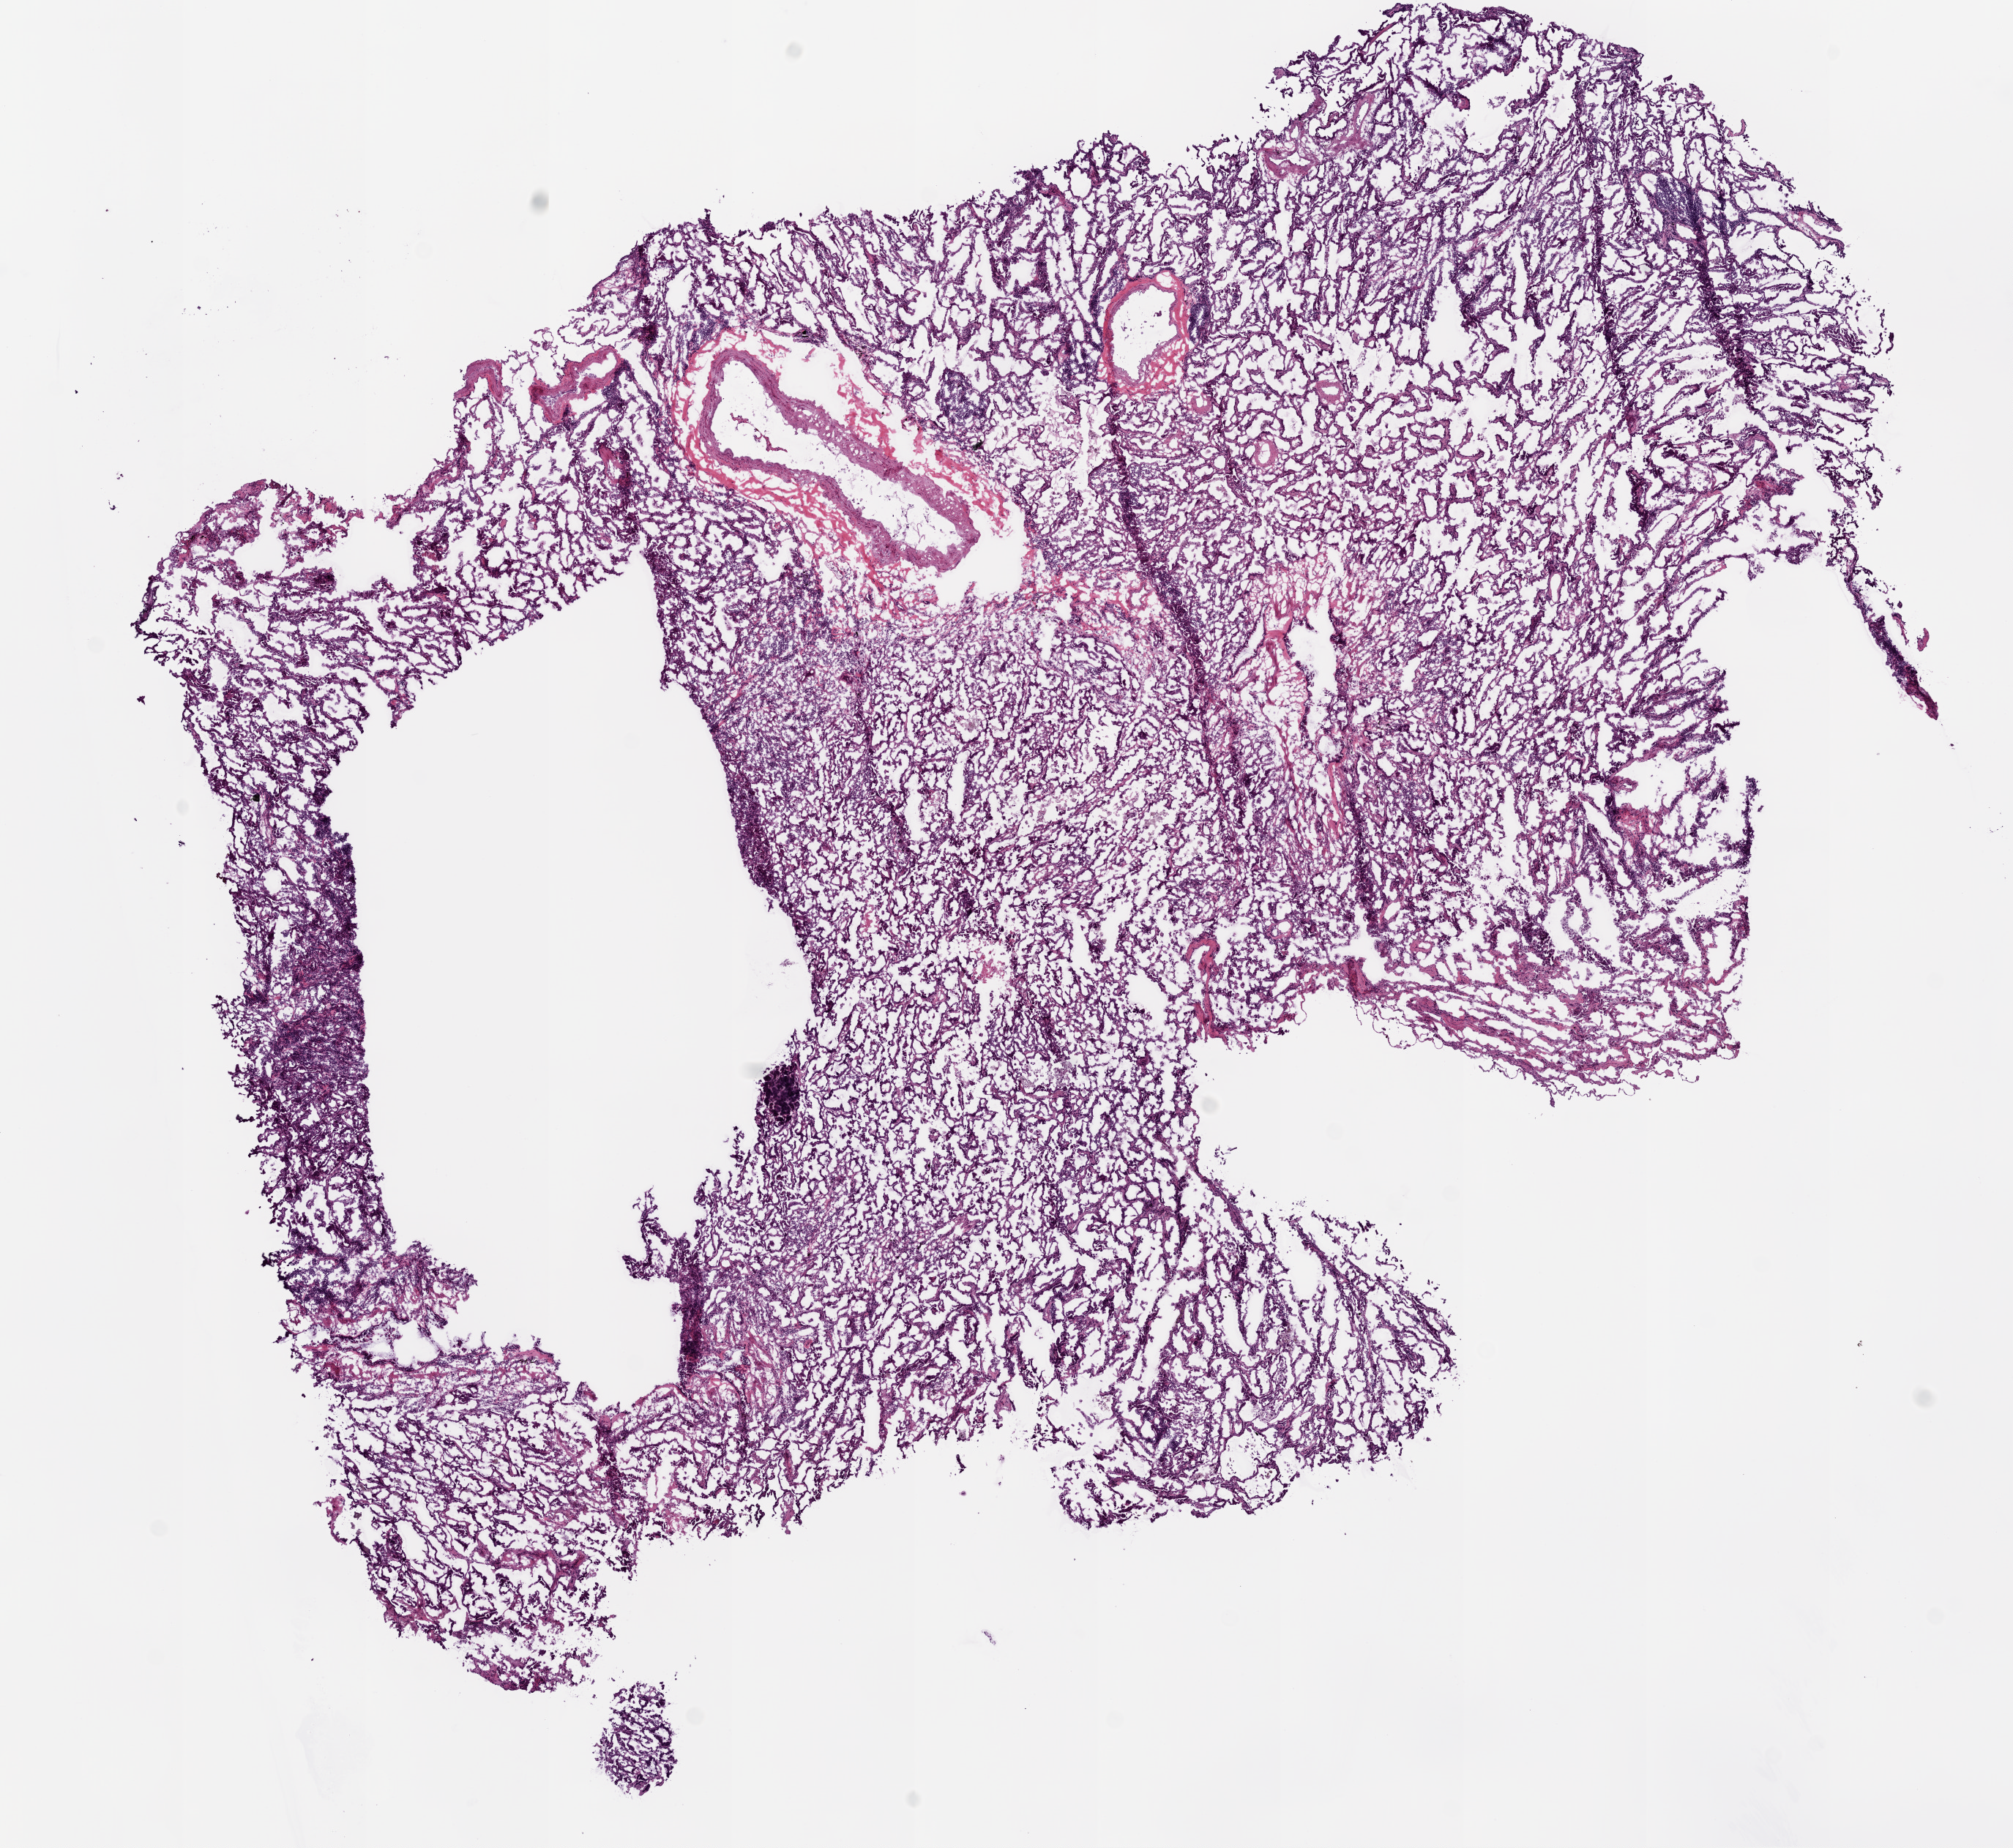
Digitized H&E-stained tissue section (whole slide) — a low-resolution overview of the entire scanned area, about 11.0 x 10.1 mm (acquisition: 20x scan), frozen section, lung, primary tumour sample. Male patient; age at initial diagnosis 60 years. Pathologist review of this section (percent, as recorded): tumour cells 90%, tumour nuclei 75%, normal cells 0%, stromal cells 10%, necrosis 0%. Inflammatory infiltration, as recorded: lymphocyte infiltration 10%, monocyte infiltration 5%, neutrophil infiltration 0%.
Pathologic diagnosis: Bronchiolo-alveolar carcinoma, non-mucinous (upper lobe, lung). Laterality: right. AJCC pathologic stage: IB (6th edition).